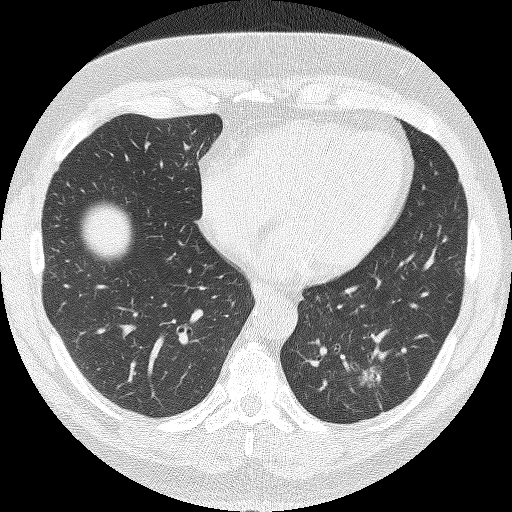
Low-dose screening chest CT, one axial slice. Slice 47 of 140 in the series (ordered by position). Reconstruction kernel FC51. 120 kVp. Lung window (W 1500 / L -600 HU). 512 × 512 image matrix, field of view 349 × 349 mm.
Structures marked on this image (manually delineated by an expert):
- lesion 1 (tumor, lower lobe of left lung): bounding box [x1, y1, x2, y2] px = [359, 367, 381, 386]